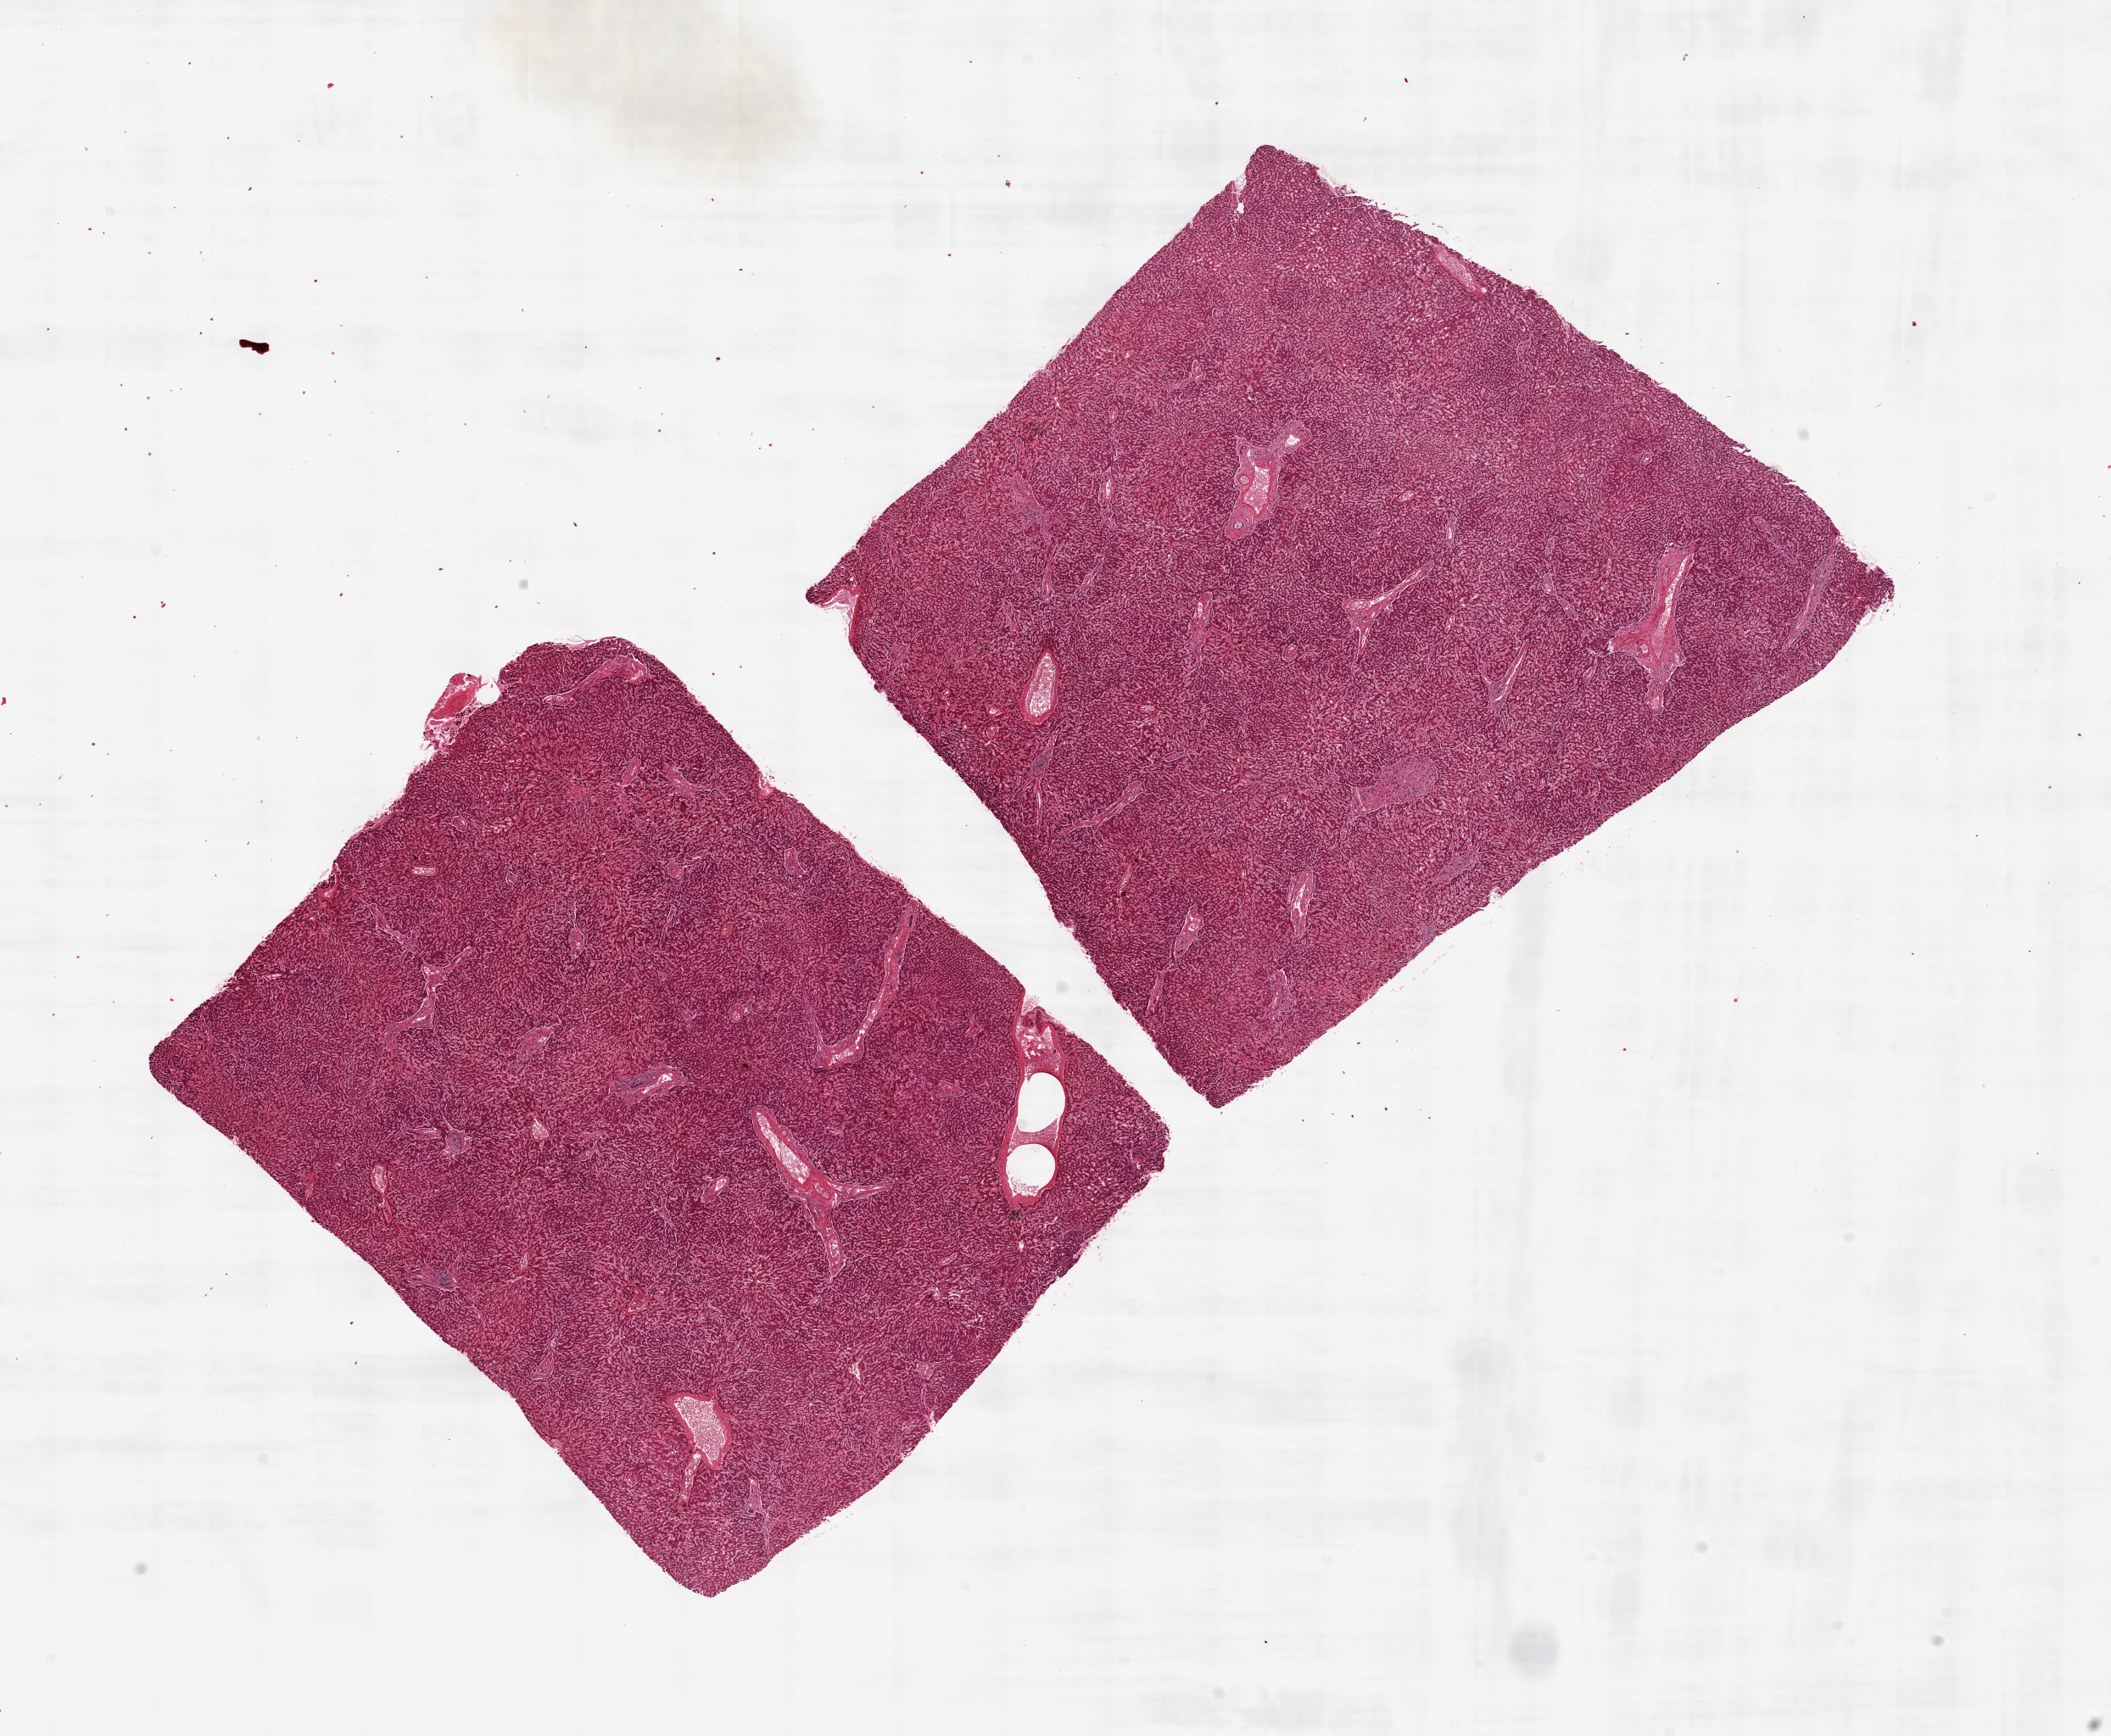
H&E whole-slide image, brightfield — whole scanned area (about 19.7 x 16.2 mm, slide scanned at 20x) shown as a low-resolution overview, PAXgene-fixed, paraffin-embedded tissue, section of liver (target tissue), tissue donor sample. Male donor.
* review note (as recorded): 2 pieces 8x6 & 7x7mm; minimal steatosis